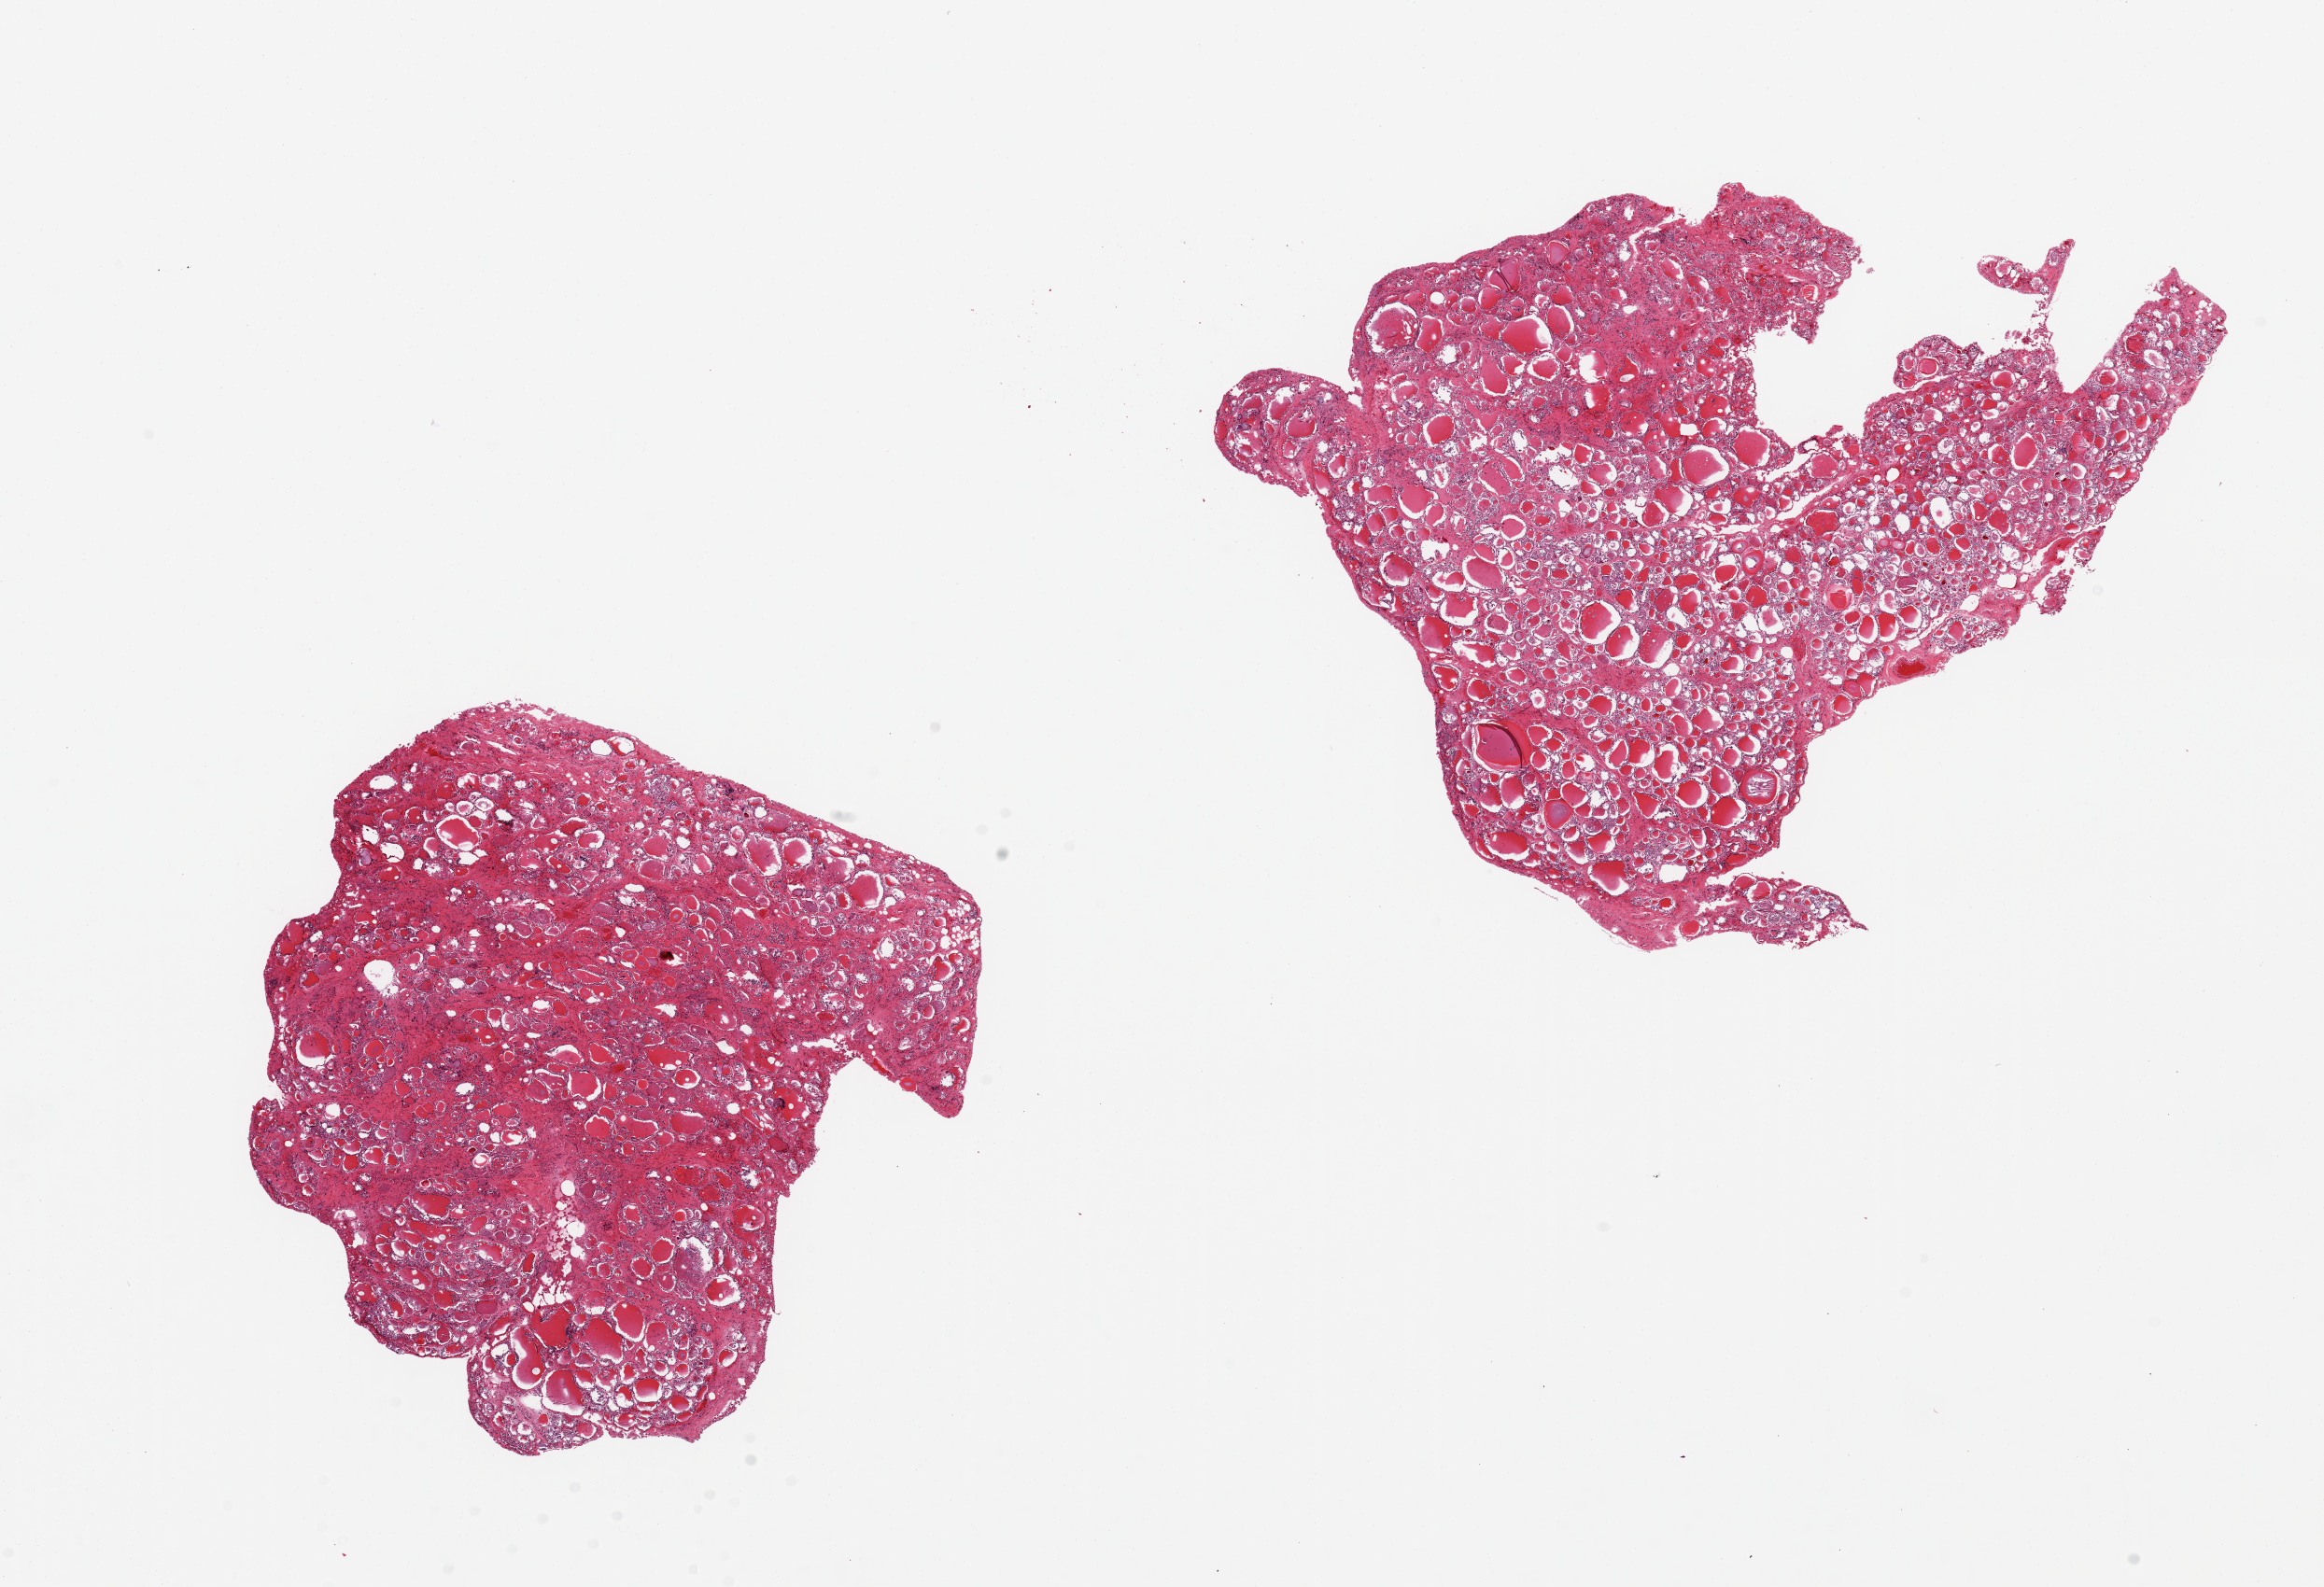
Whole-slide image, hematoxylin and eosin (H&E) stain — low-resolution overview of the scanned area, about 19.7 x 13.4 mm. PAXgene-fixed, paraffin-embedded tissue. Section of thyroid (target tissue). Tissue donor sample.
Reviewer comment on this tissue sample: 2 aliquots, ~6x6mm. Patchy regressive changes.